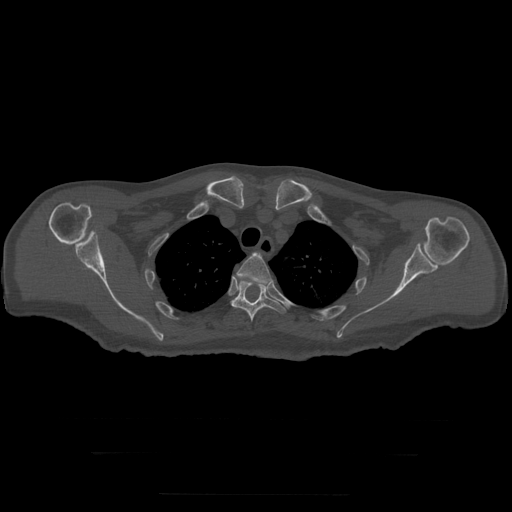
CT including the spine, one axial slice. Bone window (W 1800 / L 400 HU). 1.25 mm slice thickness. 512 × 512 image matrix, field of view 510 × 510 mm. Patient age 73 years. From the clinical record (not read from this slice): primary cancer: prostate.
Outlined on this slice (semi-automatic segmentation, software-assisted and operator-edited):
- T3 vertebra: bounding box <237,253,271,284> (left, top, right, bottom; pixels)
- T4 vertebra: <232,278,286,322>